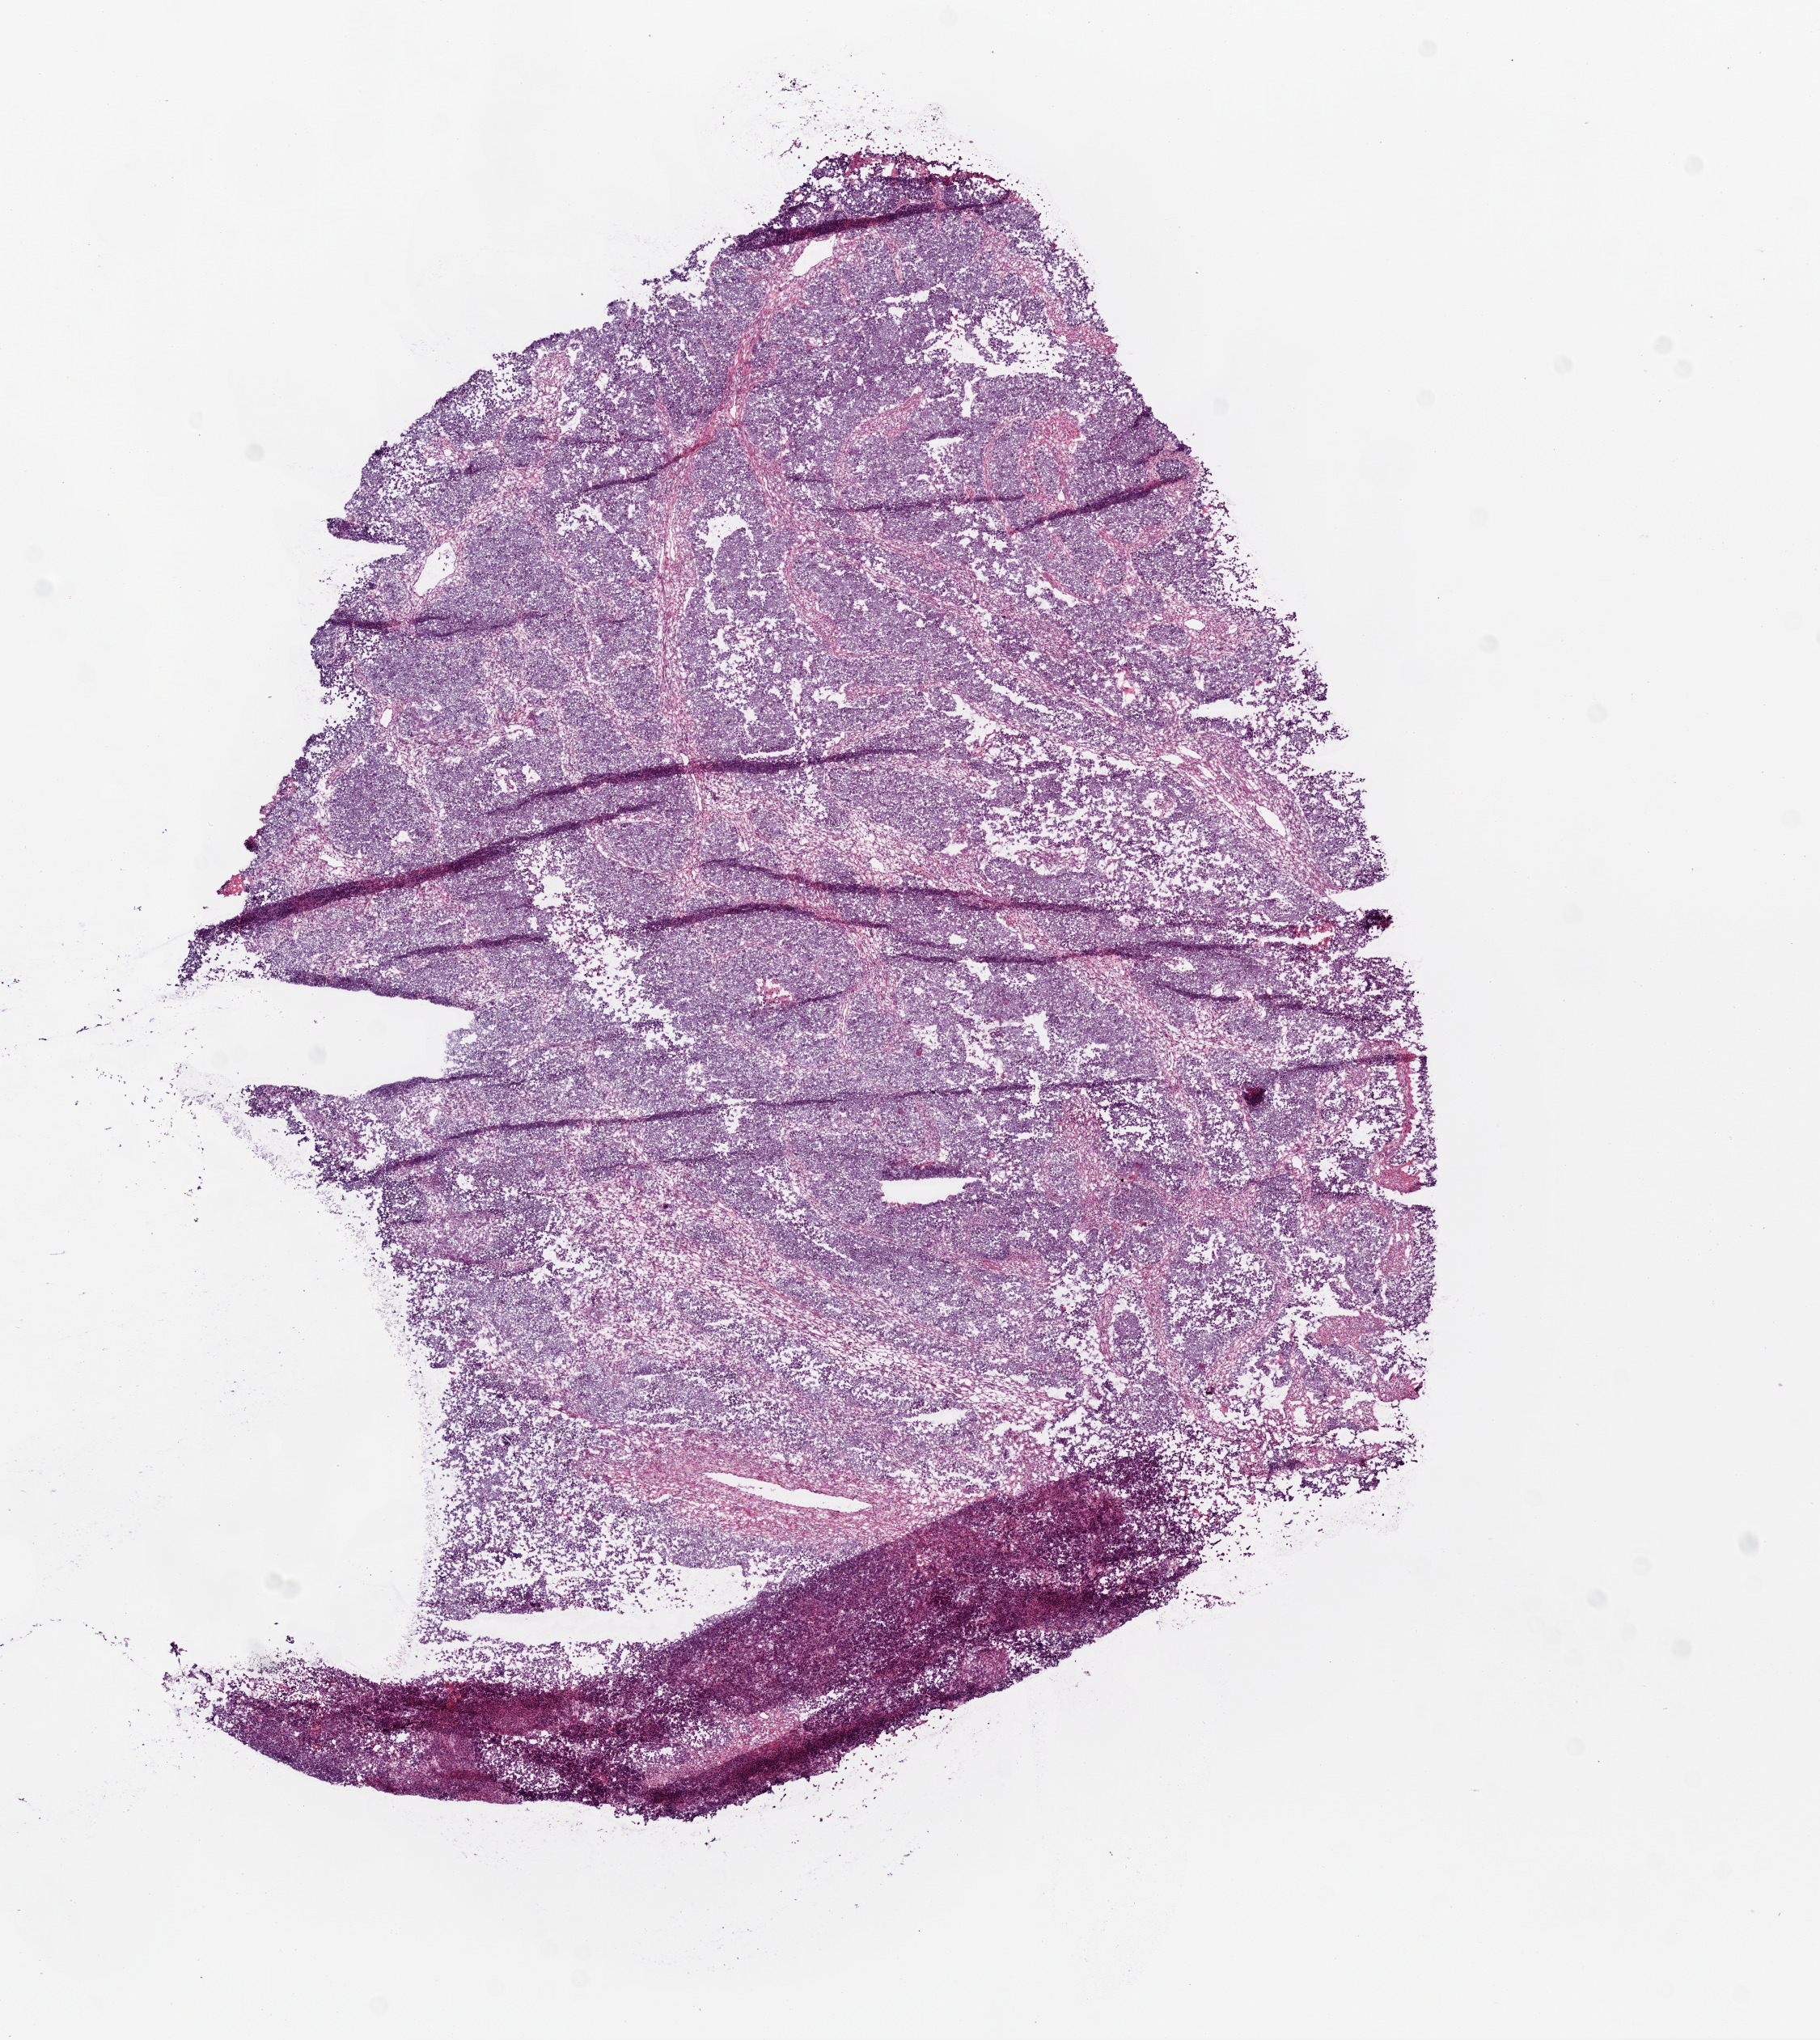
Digitized H&E tissue section (whole slide), low-resolution overview of the scanned area, about 9.0 x 10.1 mm, frozen section, ovary, primary tumour sample. Female patient; age at initial diagnosis 55 years. Histologic grade: G3 (poorly differentiated). Pathologist review of this section (percent, as recorded): tumour cells 80%, tumour nuclei 95%, normal cells 0%, stromal cells 20%, necrosis 0%.
Diagnosis: Serous surface papillary carcinoma. FIGO stage: IIIC. Laterality: bilateral.